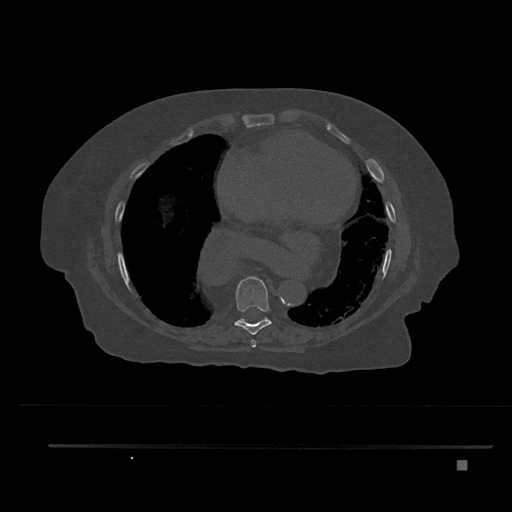
CT including the spine, one axial slice. Slice 437 of 797 in the series (ordered by position). Bone window (W 1800 / L 400 HU). 512 × 512 image matrix, field of view 437 × 437 mm. Female patient, age 76 years. Case-level facts recorded for this patient, not image findings: primary cancer: lung; vertebrae with lytic lesions (as recorded): T11, L3.
Annotated regions visible in this slice (semi-automatic segmentation, software-assisted and operator-edited):
- T7 vertebra: bounding box (x1, y1, x2, y2) in pixels: (251, 340, 256, 347)
- T8 vertebra: (234, 277, 272, 335)
- T9 vertebra: (240, 319, 245, 321)